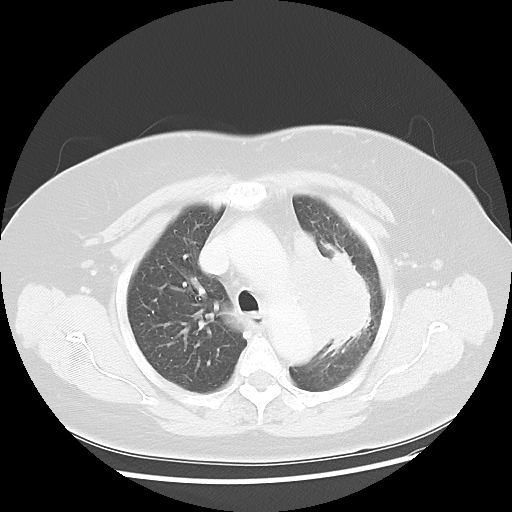
Chest CT, one axial slice. Position 35 of 49 along the scan axis. Reconstruction kernel LUNG. Lung window (W 1500 / L -600 HU). 512 × 512 image matrix. Female patient, age 58 years. From the clinical record (not read from this slice): clinical TNM (as recorded): T4 N3 M0; histopathological grade: G3.
Outlined on this slice (rectangle marked by the reading radiologist):
- lung tumour (recorded histology: small cell carcinoma): bounding box (x1, y1, x2, y2) in pixels: (275, 223, 383, 364)